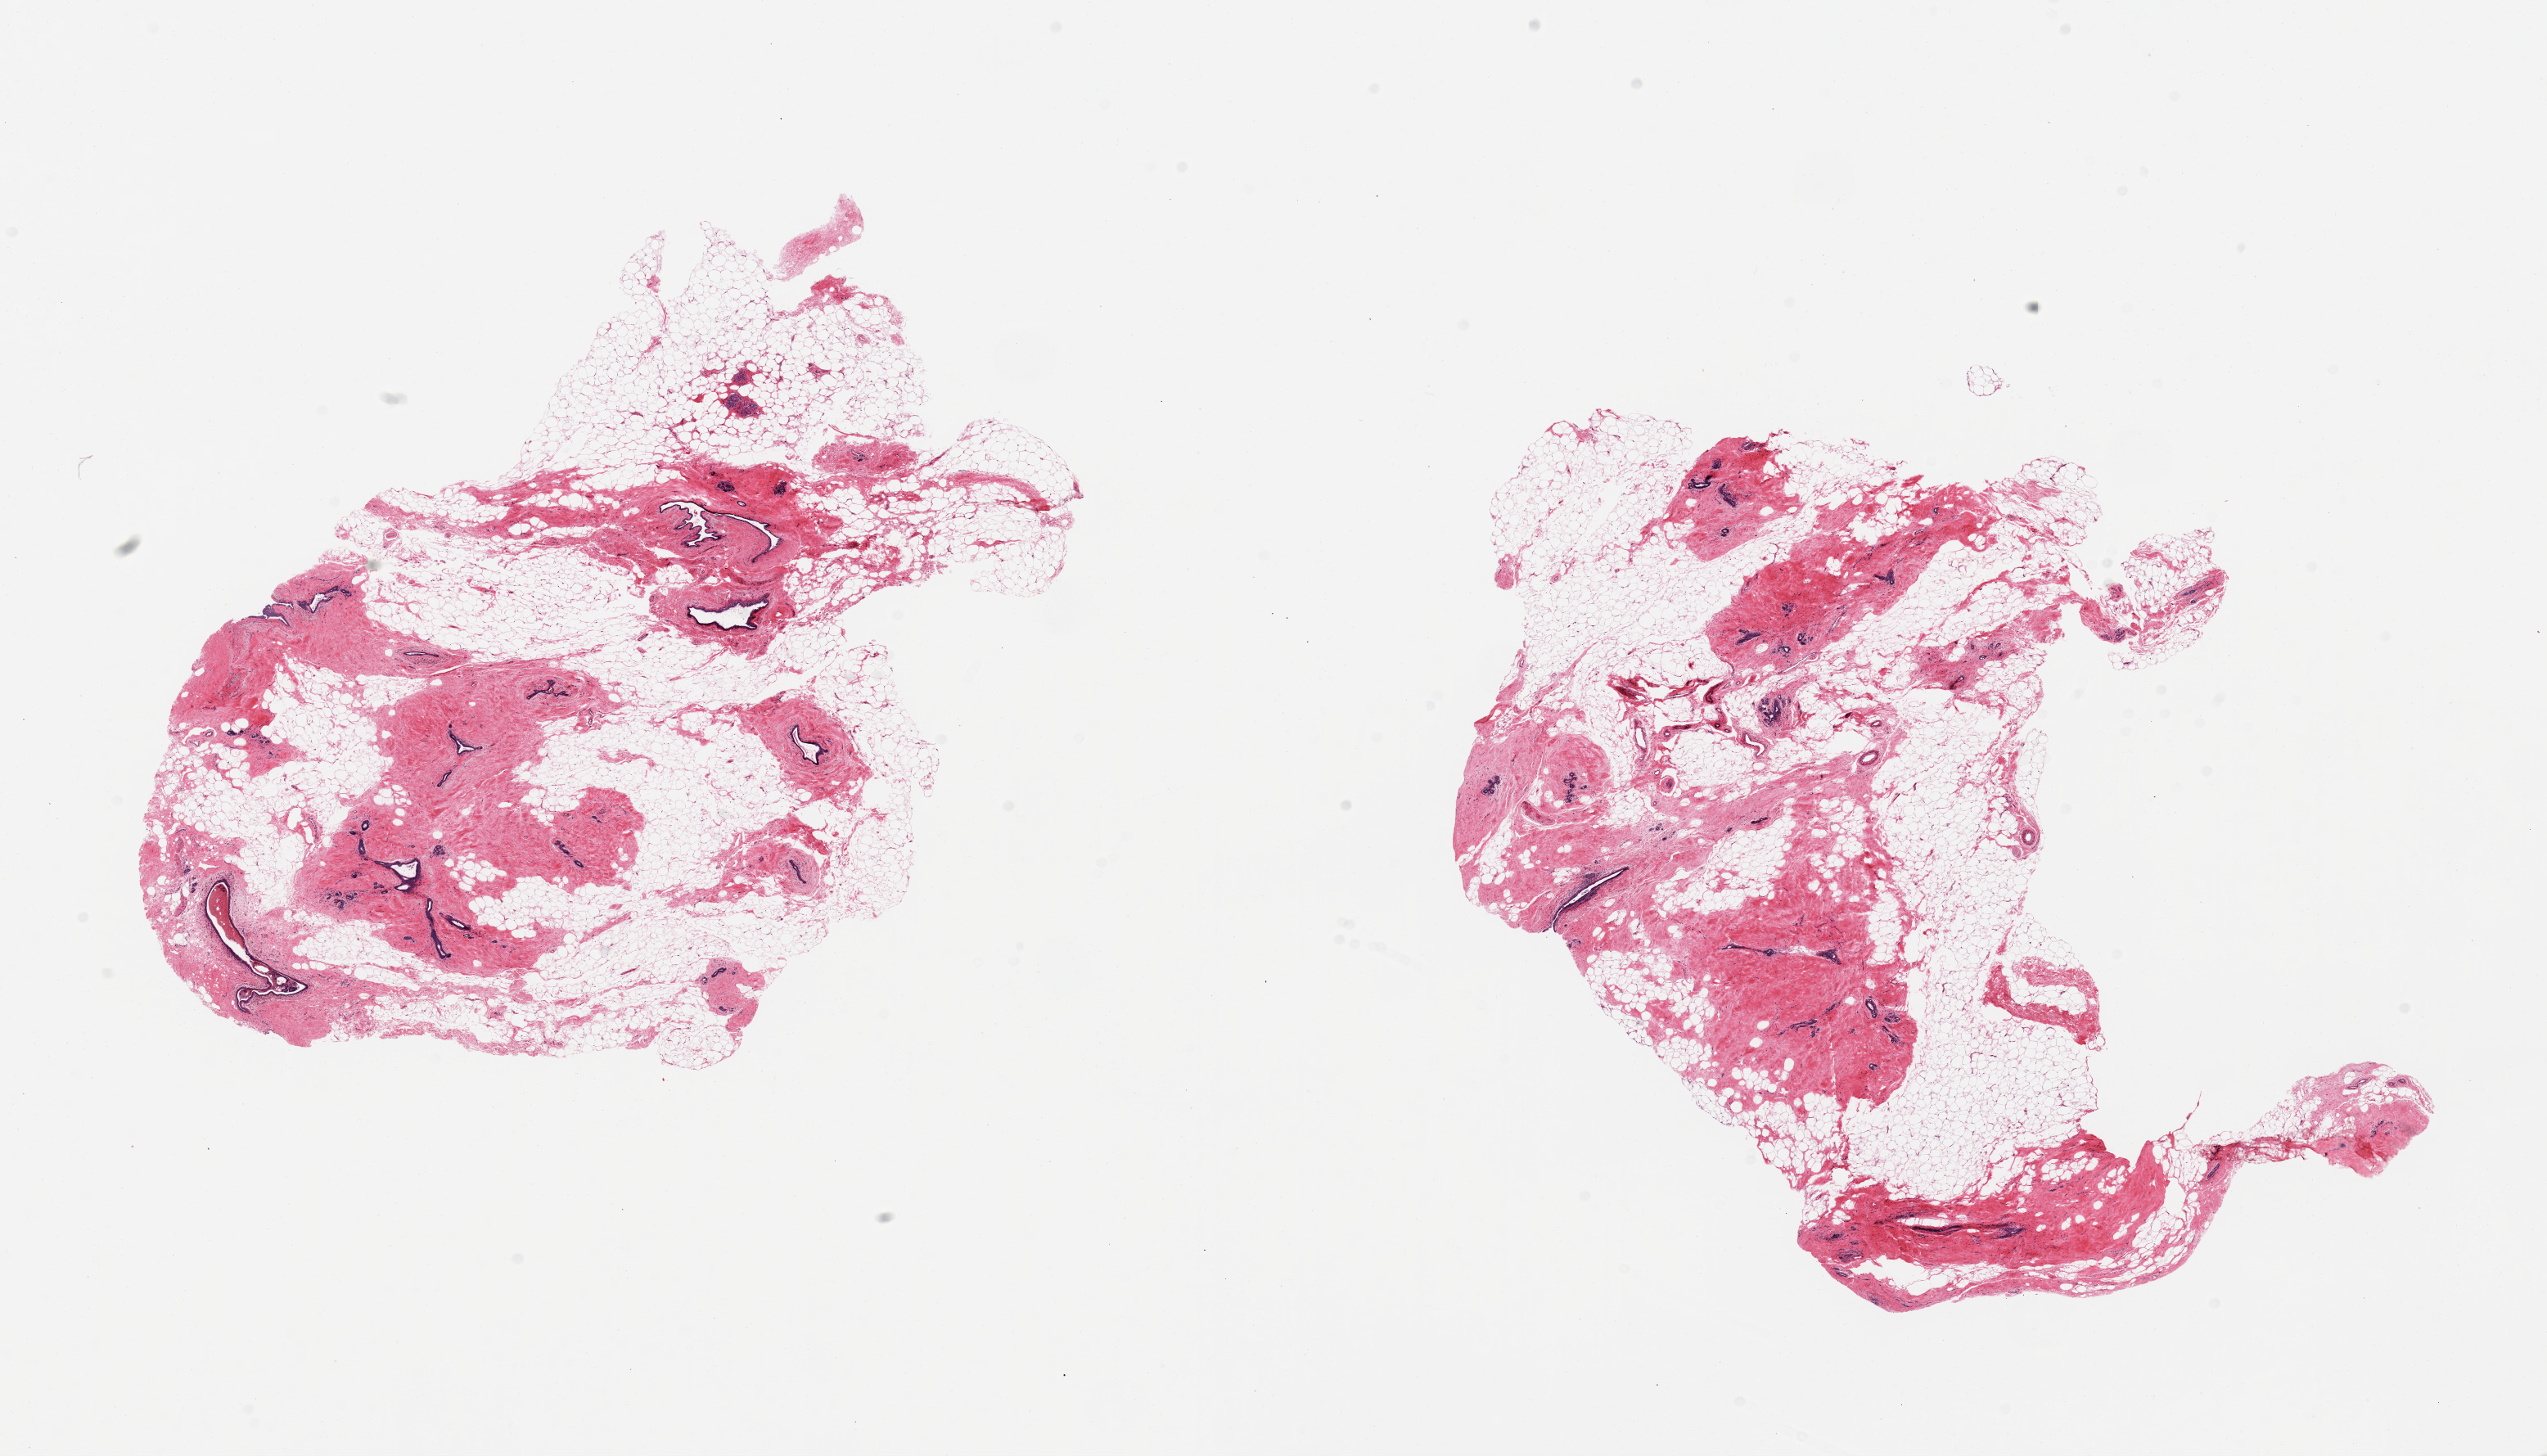
Hematoxylin and eosin (H&E) whole-slide image, brightfield, low-resolution overview of the scanned area, about 24.6 x 14.1 mm (acquisition: 20x scan). PAXgene-fixed paraffin-embedded (PFPE) section. Section of breast (target tissue). Tissue donor sample. Female donor.
Reviewer comment on this tissue sample: 2 pieces; ducts and atrophic lobules; 50% adipose.